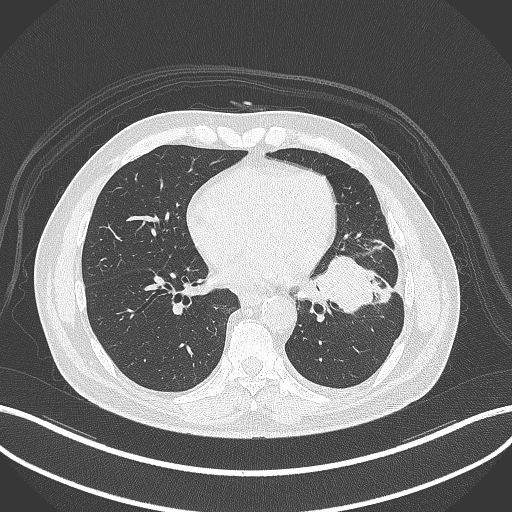
Chest CT, one axial slice. Reconstruction kernel B70f. 120 kVp. Lung window (W 1500 / L -600 HU). 512 × 512 image matrix. Male patient, age 68 years. From the clinical record (not read from this slice): clinical TNM (as recorded): T2b N0 M0.
Outlined on this slice (bounding box drawn by a radiologist):
- lung tumour (recorded histology: squamous cell carcinoma): bounding box [x1, y1, x2, y2] px = [311, 251, 380, 319]